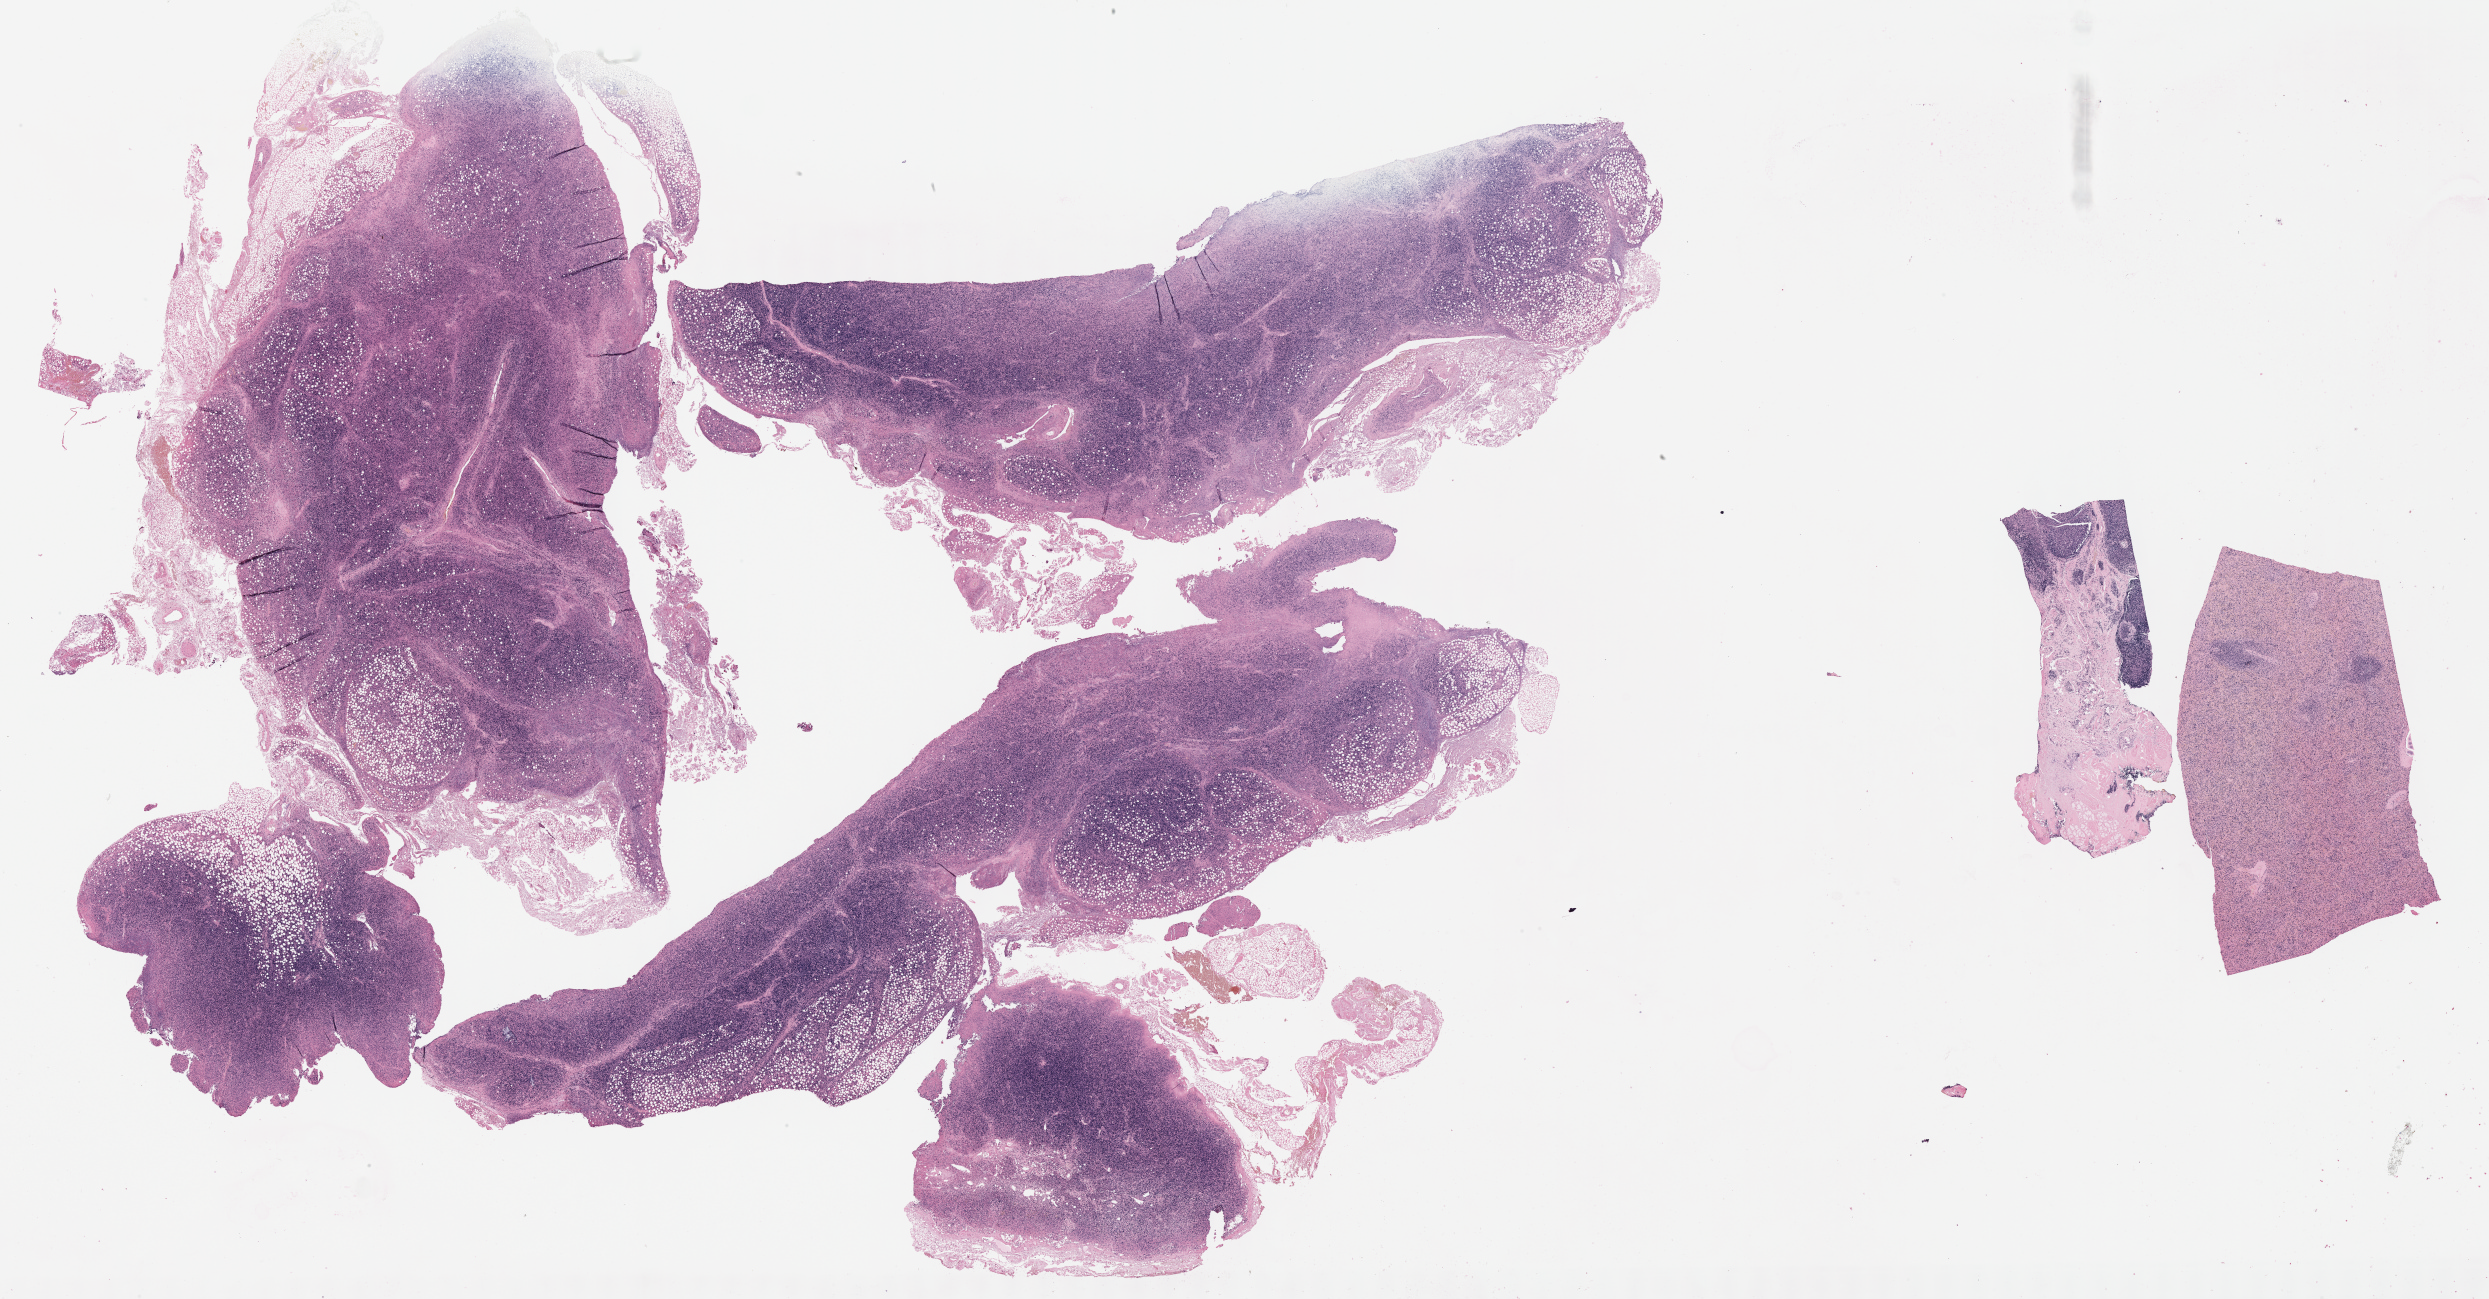
Whole-slide image; stain recorded as Iodonitrotetrazolium — a low-resolution overview of the entire scanned area, about 40.3 x 21.0 mm. Specimen: tumor tissue. Site: lymph node. Patient male; 68 years old.
Histologic diagnosis: Diffuse large B-cell lymphoma, NOS.